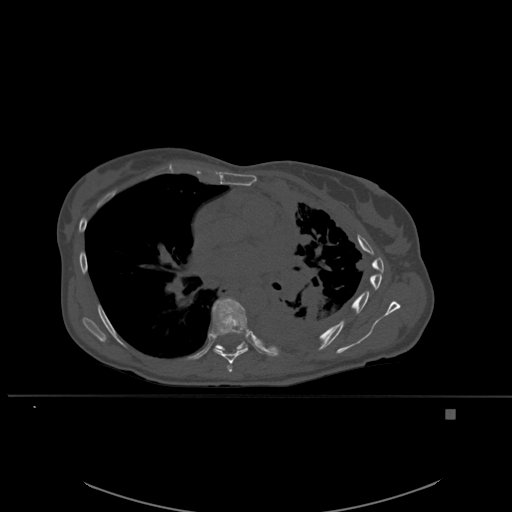
CT including the spine, one axial slice. Position 362 of 537 along the scan axis. Bone window (W 1800 / L 400 HU). 1.5 mm slice thickness. 512 × 512 image matrix, field of view 440 × 440 mm. Patient: female, 45 years. From the clinical record (not read from this slice): primary cancer: lung.
Structures marked on this image (semi-automatically segmented with operator editing):
- T6 vertebra: bounding box (x1, y1, x2, y2) in pixels: (227, 362, 233, 372)
- T7 vertebra: (212, 298, 248, 363)
- T8 vertebra: (212, 329, 248, 353)